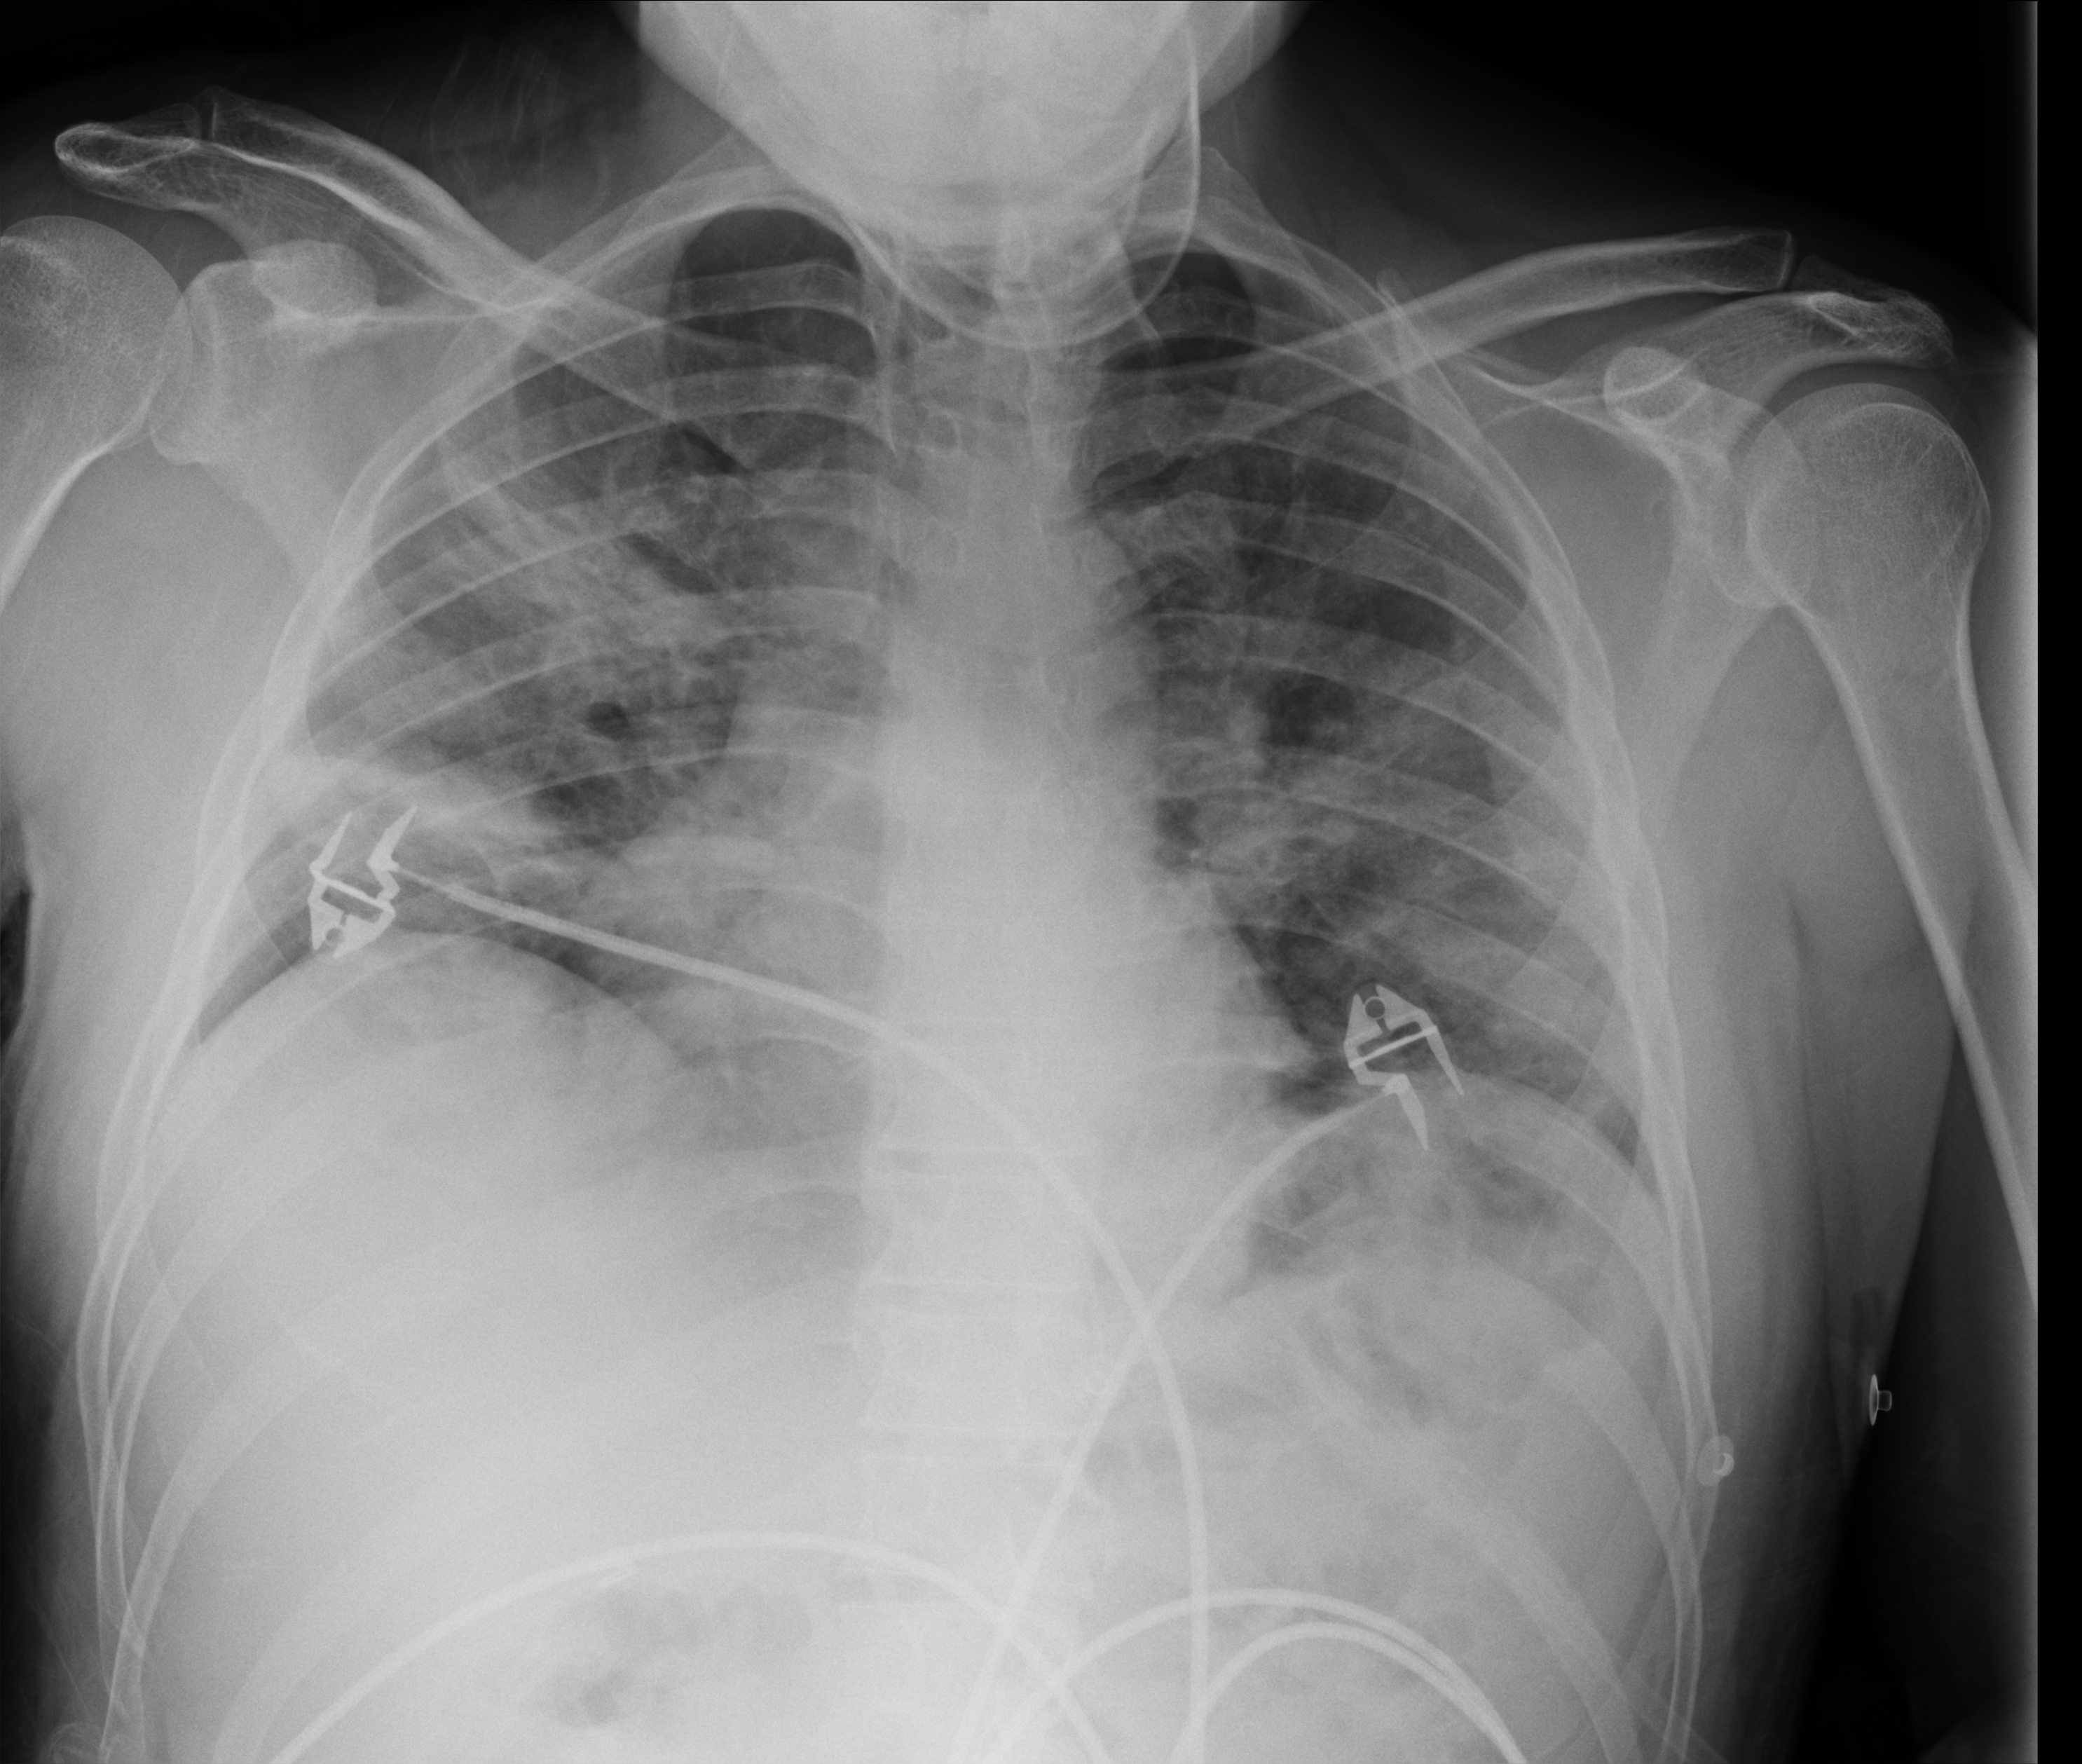
Chest X-ray (portable). Male patient hospitalised with COVID-19, age 18–59 years.
From the hospital-stay record, not from the radiograph (when in the stay this image was taken is not recorded): admitted to intensive care during this hospital stay: yes; mechanically ventilated during this hospital stay: yes; COPD (admission record): no.